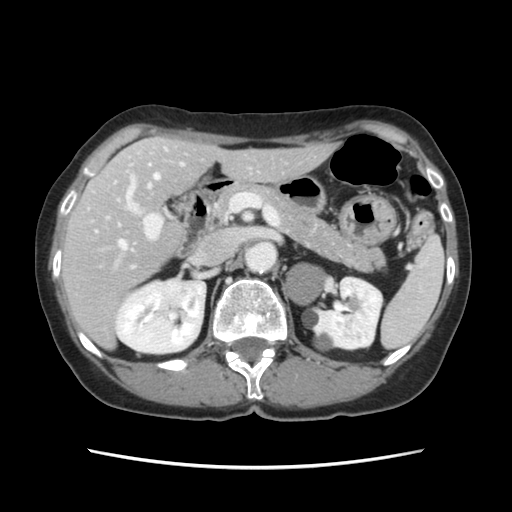
Contrast-enhanced abdominal CT, one axial slice. Position 69 of 120 along the scan axis. Intravenous contrast given. Soft-tissue window (W 400 / L 40 HU). 2.5 mm slice thickness. 512 × 512 image matrix. Female patient, age 70 years. Case-level facts recorded for this patient, not image findings: diagnosis: colorectal cancer liver metastases, imaged before liver resection.
Outlined on this slice (outlined manually by an expert reader):
- hepatic veins: bounding box [x1, y1, x2, y2] px = [119, 174, 159, 250]
- liver: [63, 138, 333, 346]
- planned liver remnant (the part of the liver to remain after resection): [86, 138, 333, 278]
- portal vein (with intrahepatic branches): [106, 148, 184, 268]